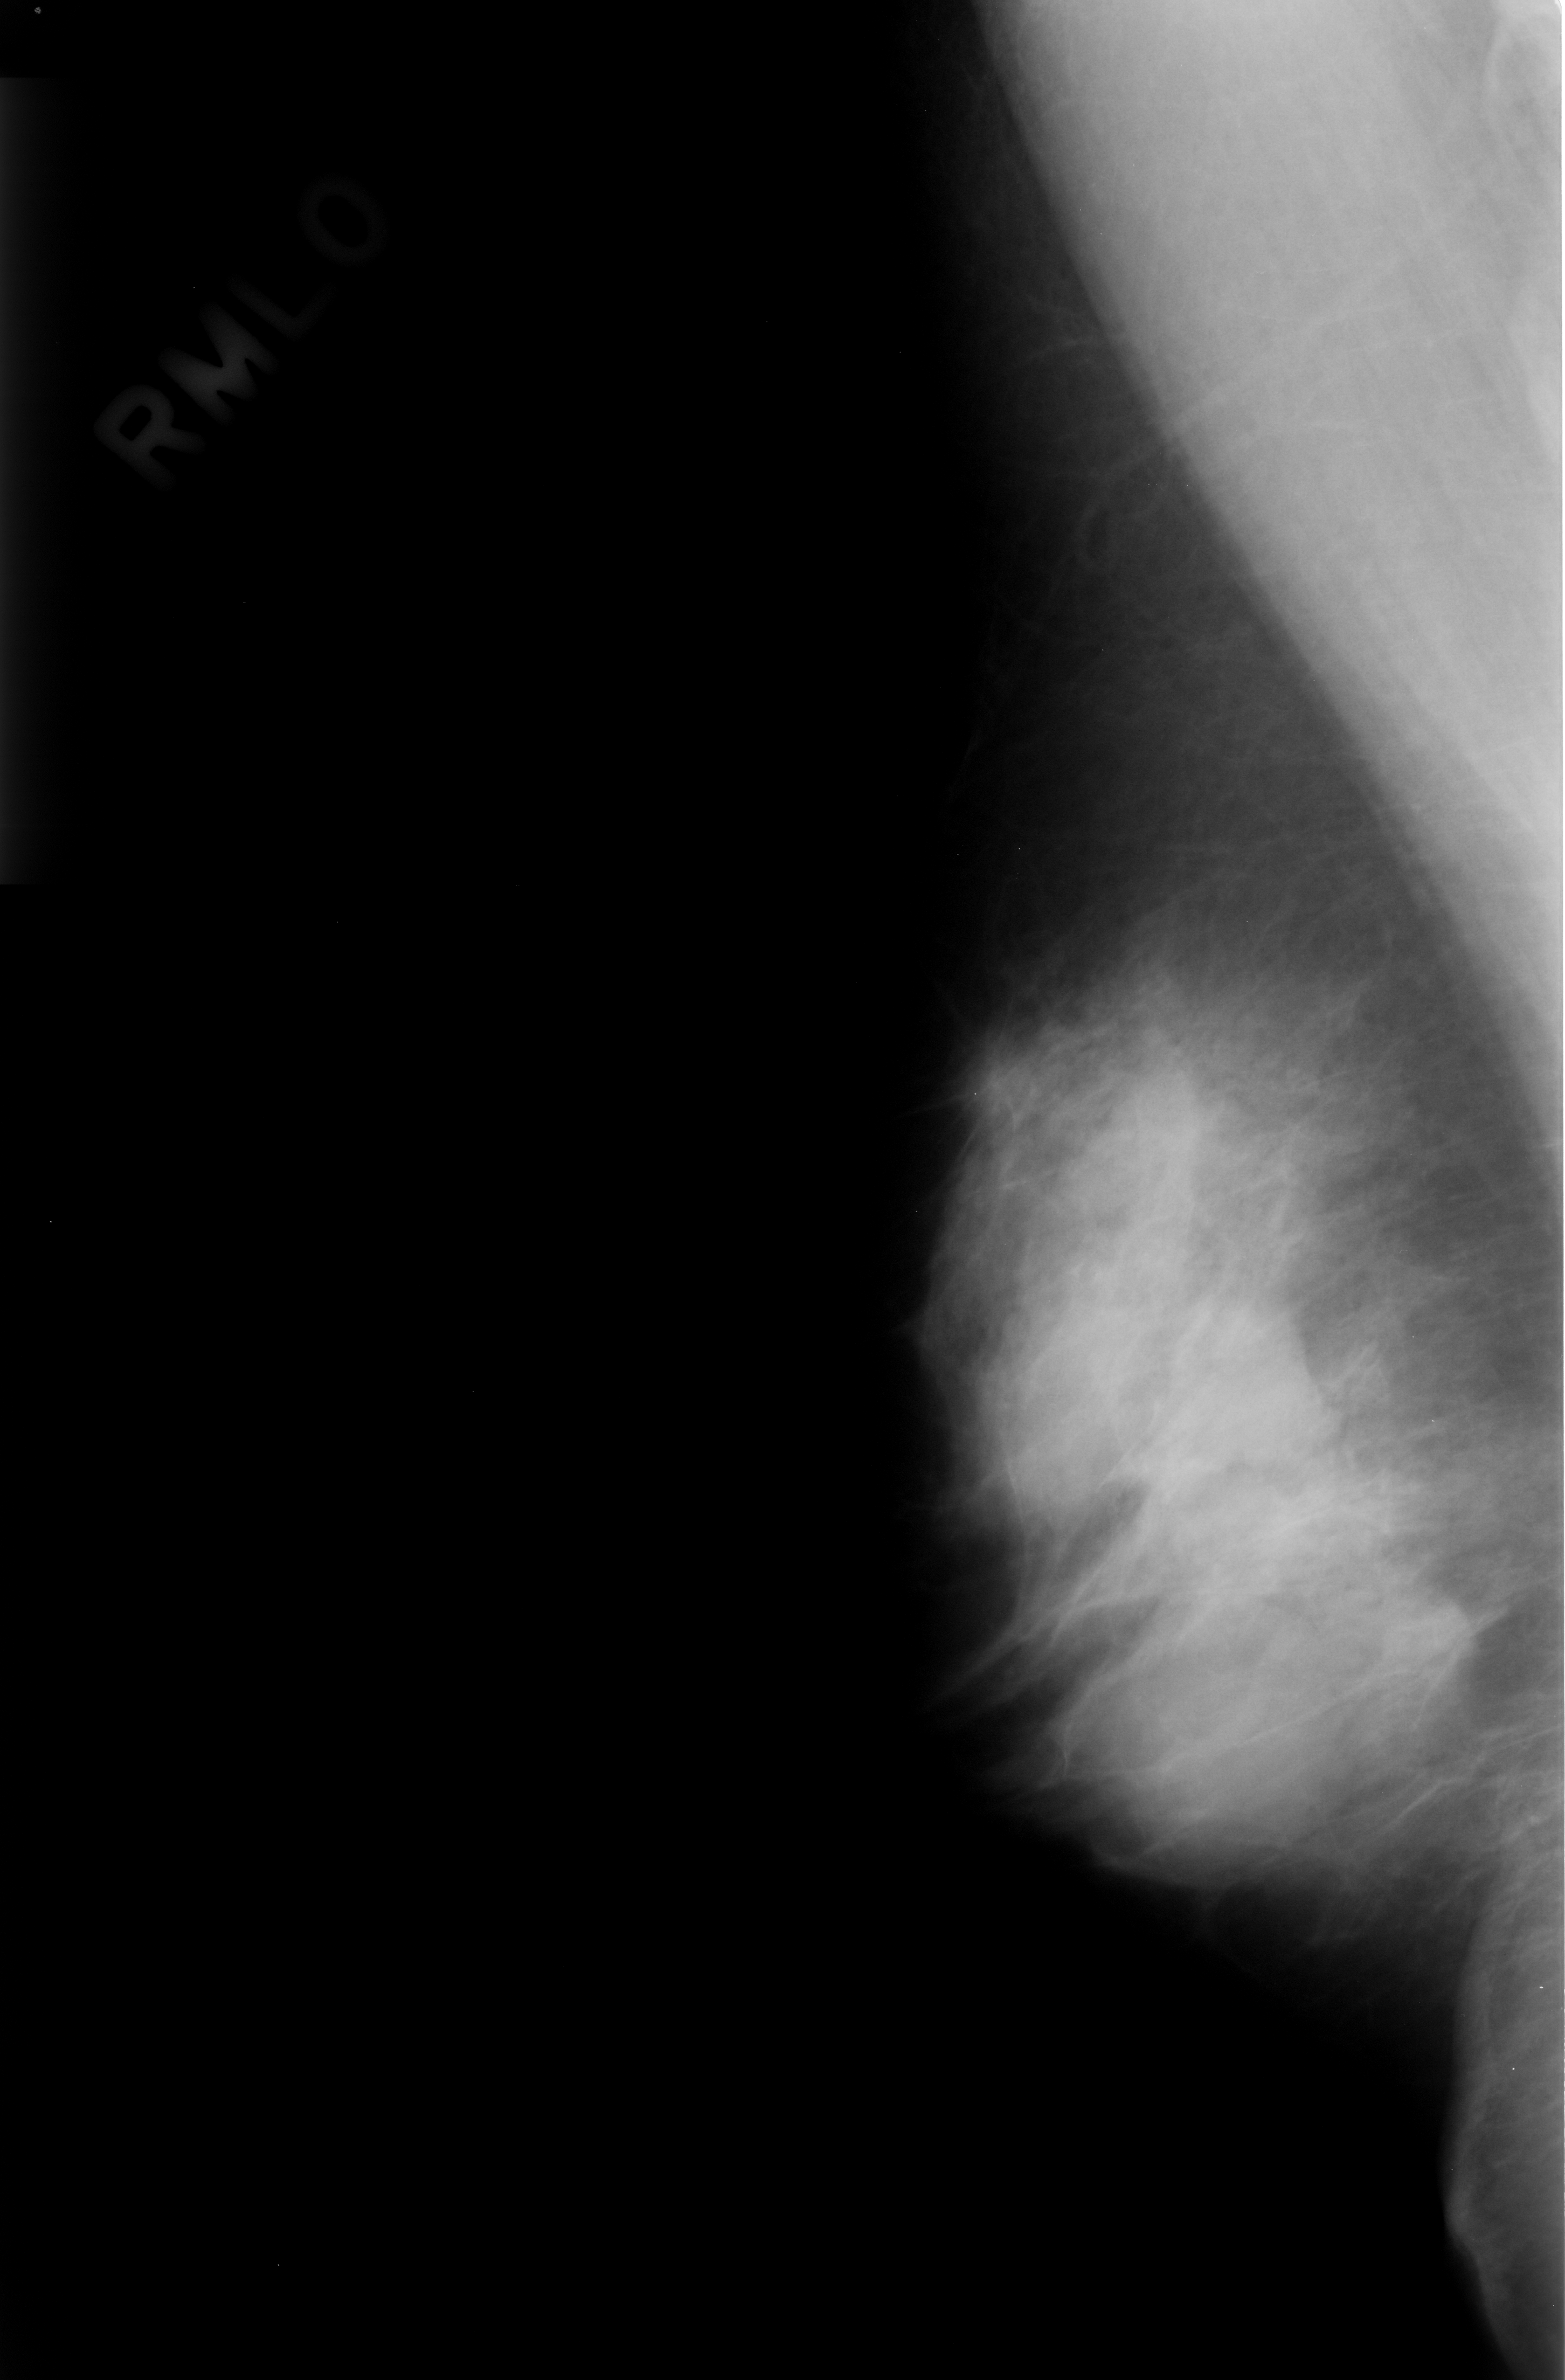
Digitized screen-film mammogram; right breast; MLO view; BI-RADS breast density category 4 (scale 1–4); 1565 × 2380 image matrix.
Marked abnormalities (boxes around the expert regions of interest):
- mass, shape lobulated, margins obscured; BI-RADS assessment category 3; pathology (as recorded): benign: bounding box [x1, y1, x2, y2] px = [1050, 1604, 1360, 1905]